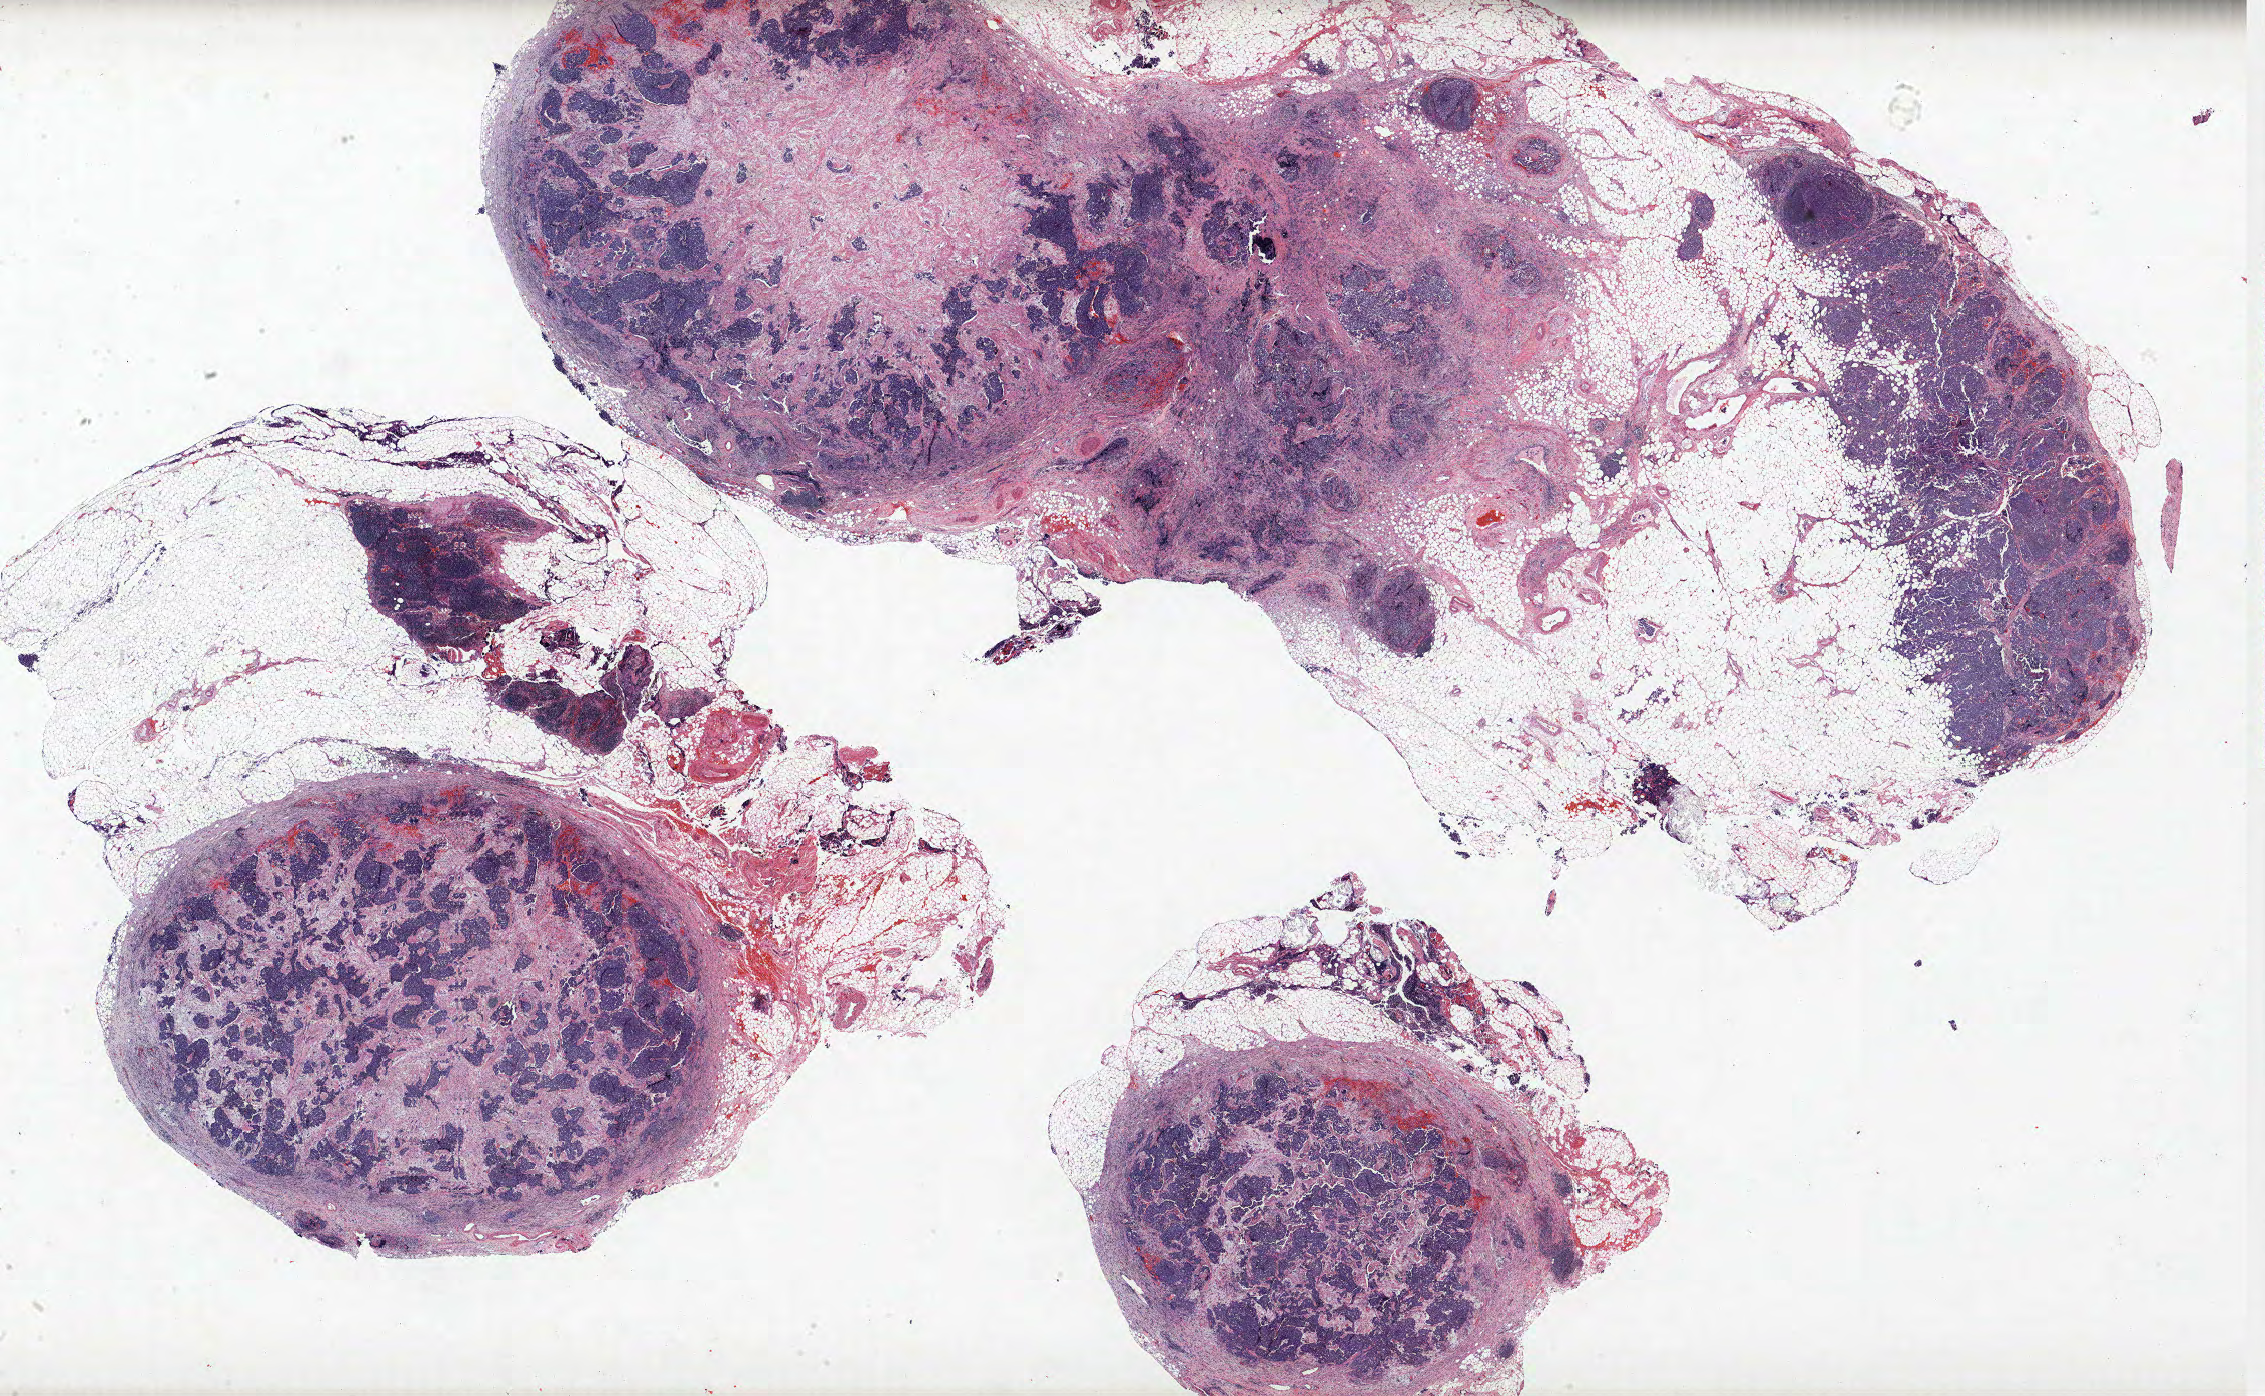
Whole-slide histology image, H&E-stained, low-resolution overview of the scanned area, about 36.2 x 22.3 mm; FFPE section; lung. Male patient, aged 73 at enrolment. Grade: cannot be assessed (GX).
- stage (AJCC 6th edition): IIIB
- tumour size (pathology): 19 mm
- participant's lung-cancer diagnosis: Small cell carcinoma, NOS
- primary tumour location (clinical record): left upper lobe